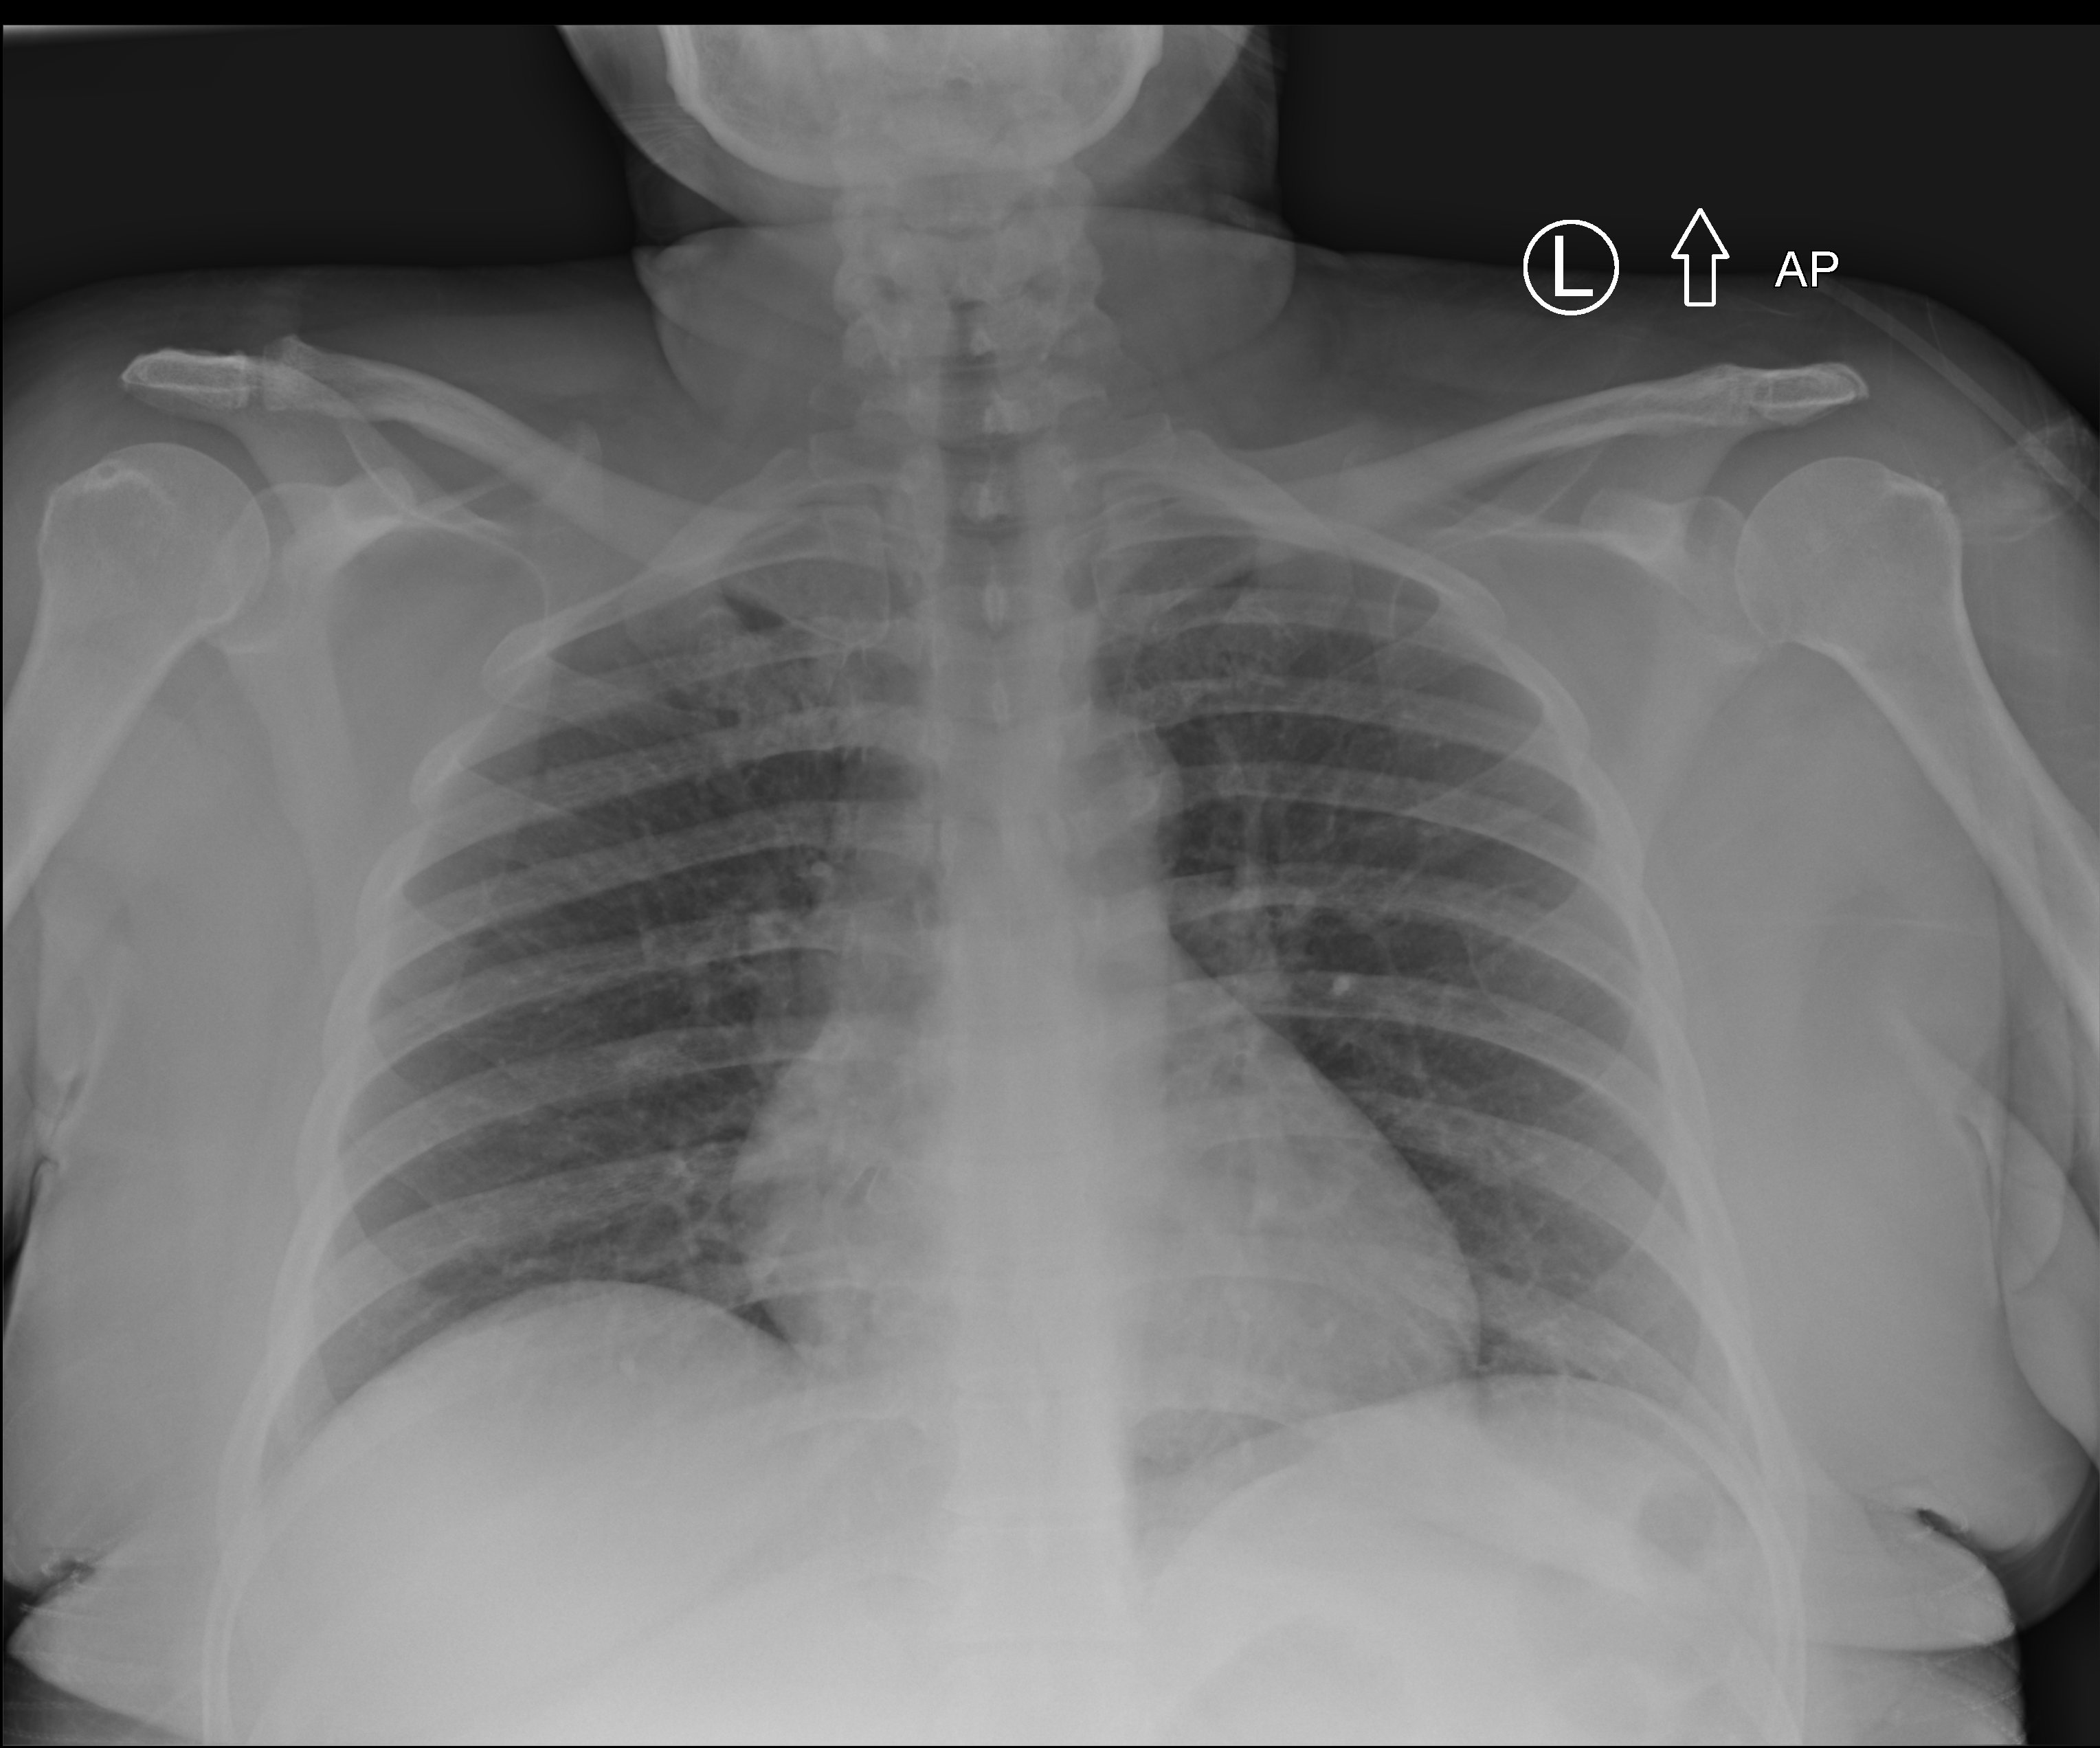
Chest radiograph (computed radiography); anteroposterior (AP) projection. Female patient hospitalised with COVID-19, age 18–59 years.
Admission-level facts for this patient (not findings on this image; timing relative to this image not recorded): other chronic lung disease (admission record): no.